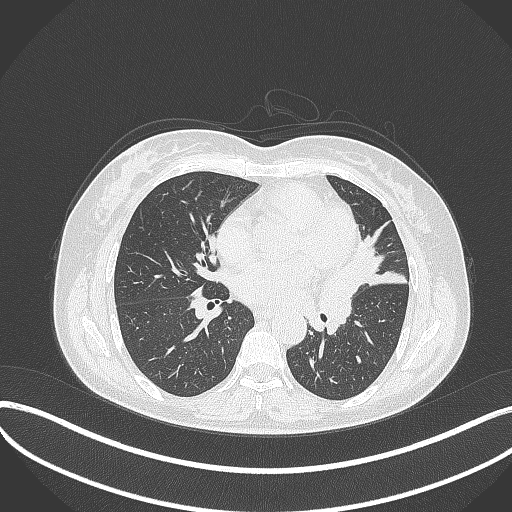
Chest CT, one axial slice. Slice 169 of 373 in the series (ordered by position). Reconstruction kernel B70f. 120 kVp. Lung window (W 1500 / L -600 HU). 512 × 512 image matrix. Patient: female, 54 years. From the clinical record (not read from this slice): clinical TNM (as recorded): T2a N1 M0; histopathological grade: G3.
Annotated regions visible in this slice (rectangle marked by the reading radiologist):
- lung tumour (recorded histology: small cell carcinoma): bounding box <314,260,360,325> (left, top, right, bottom; pixels)